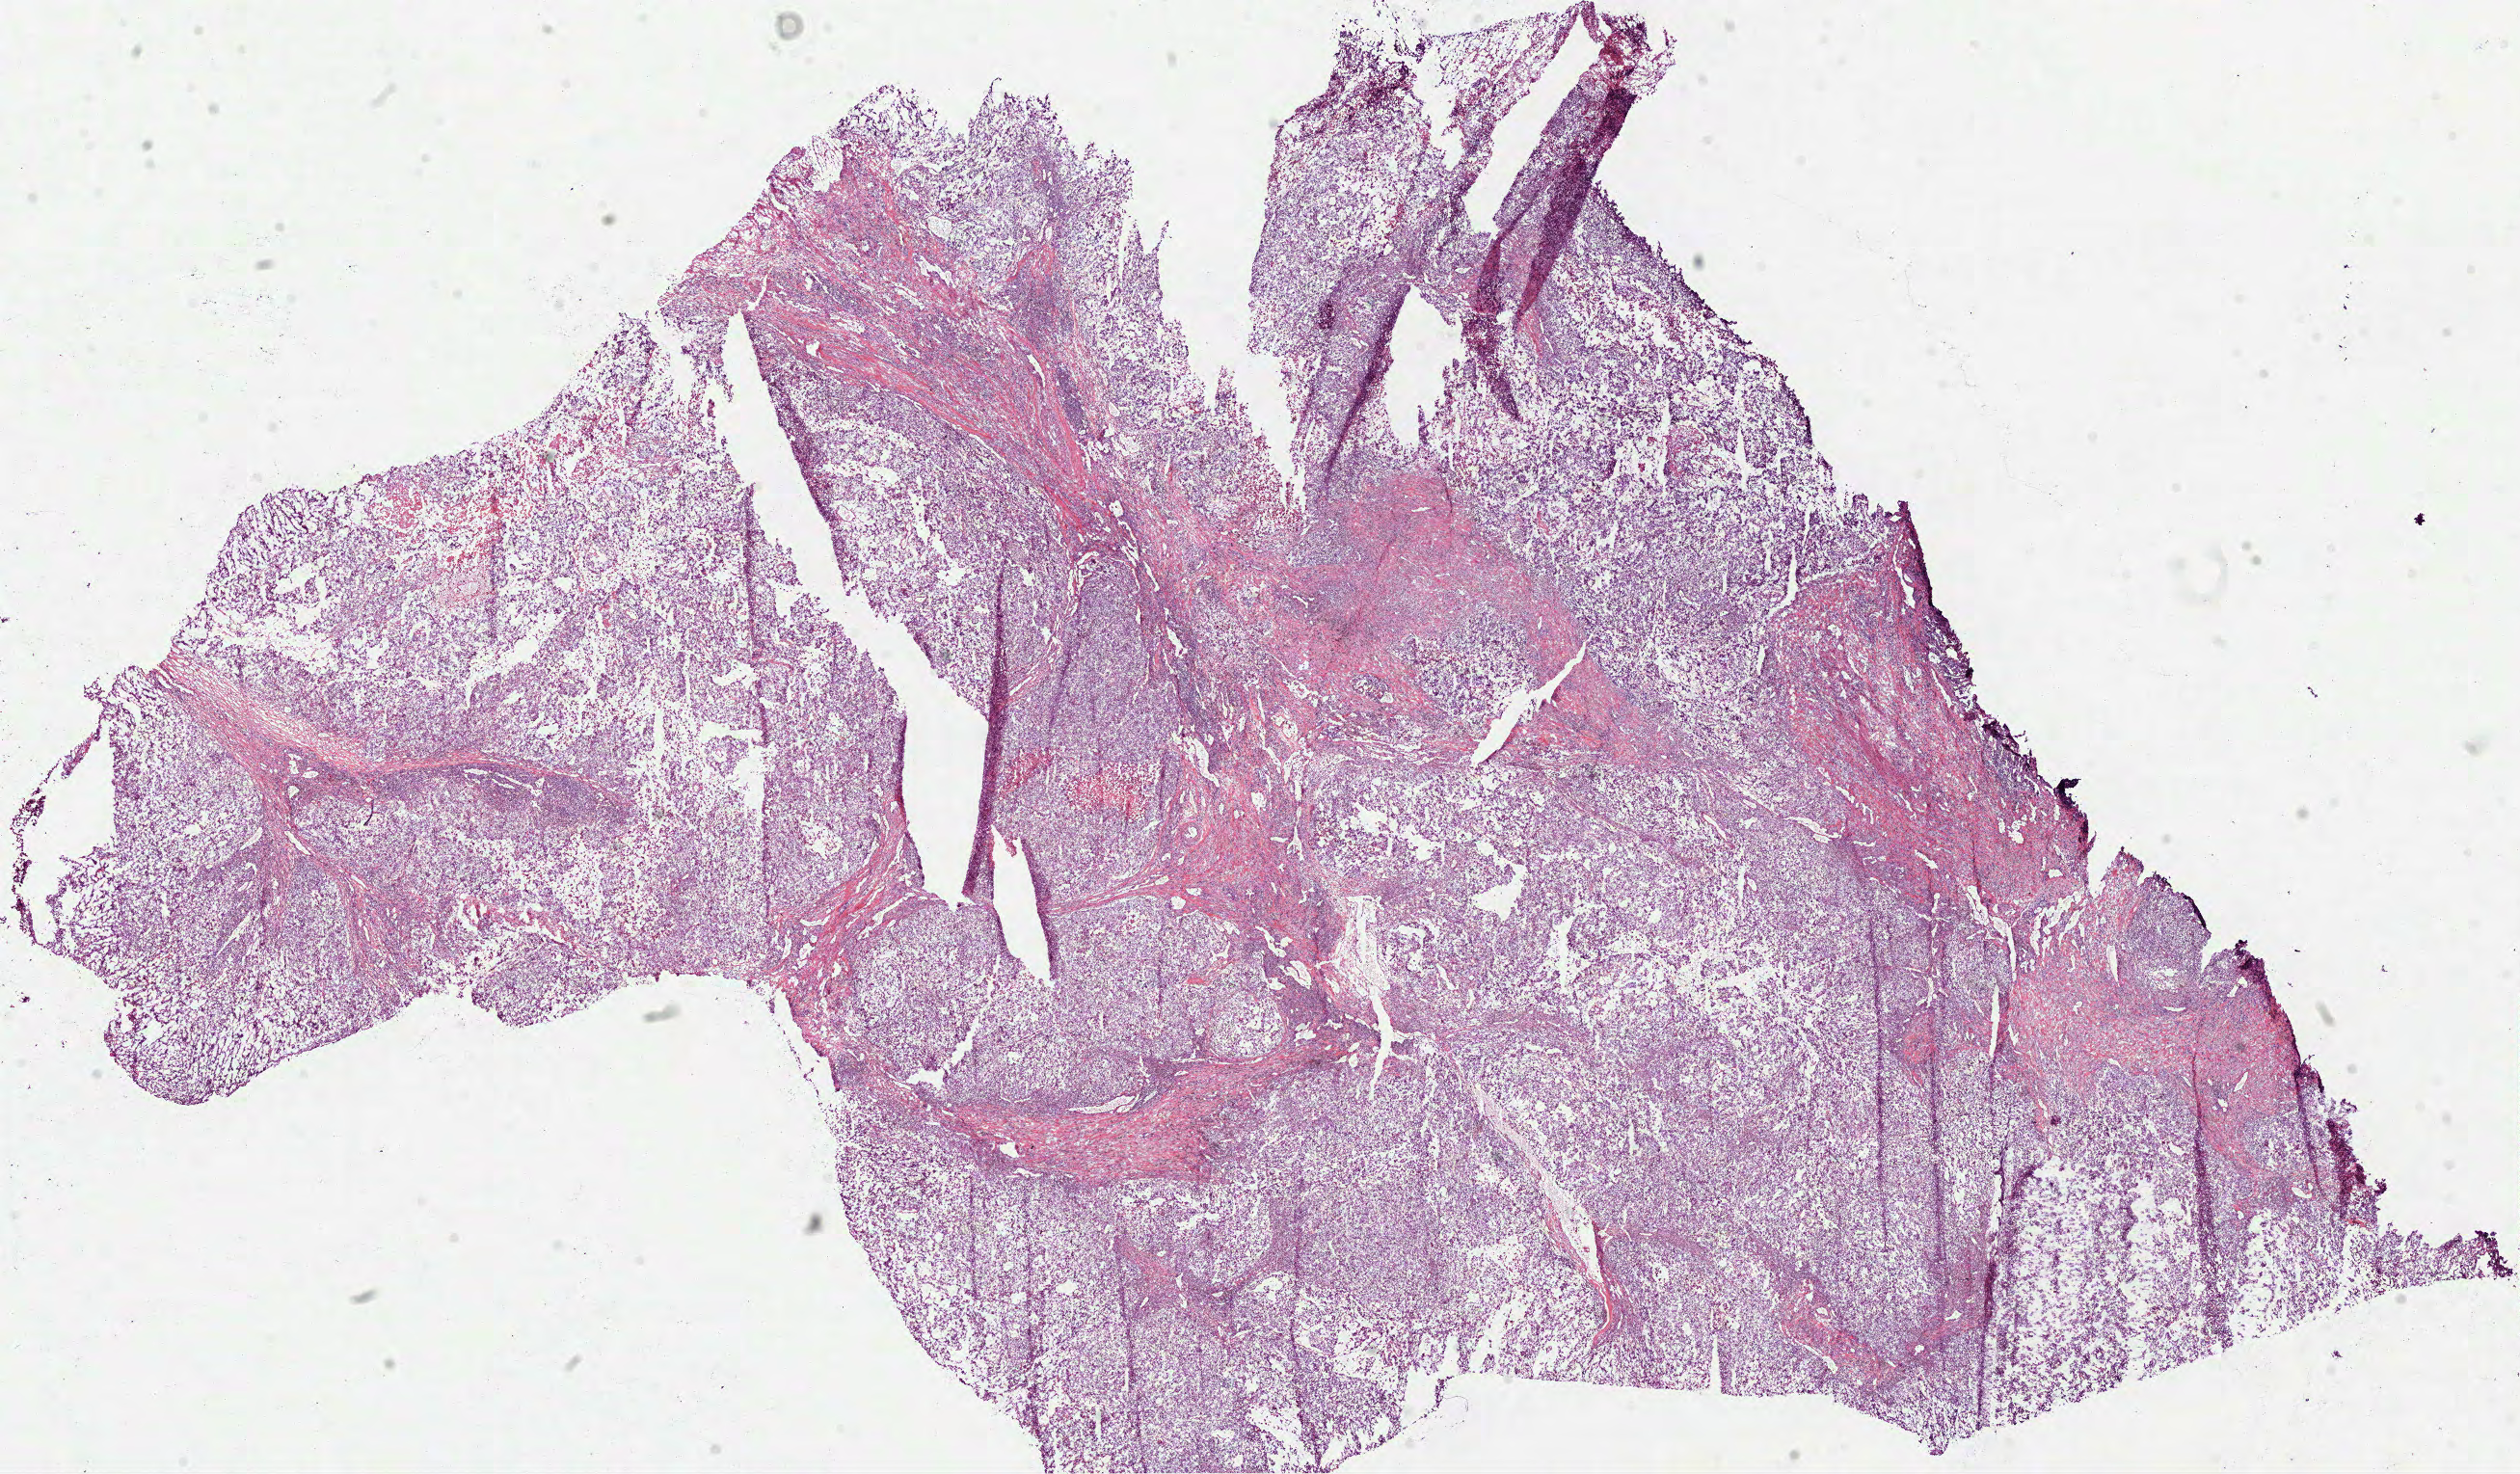
Whole-slide histology image, H&E-stained, whole scanned area (about 21.1 x 12.3 mm, from a 40x scan) shown as a low-resolution overview; frozen section; sample: primary tumour, lung. Male patient; age at initial diagnosis 59 years. Pathologist review of this section (percent, as recorded): tumour cells 80%, tumour nuclei 85%, normal cells 0%, stromal cells 15%, necrosis 5%.
Laterality: right. Diagnosis: Squamous cell carcinoma, NOS. AJCC pathologic stage: IIA.